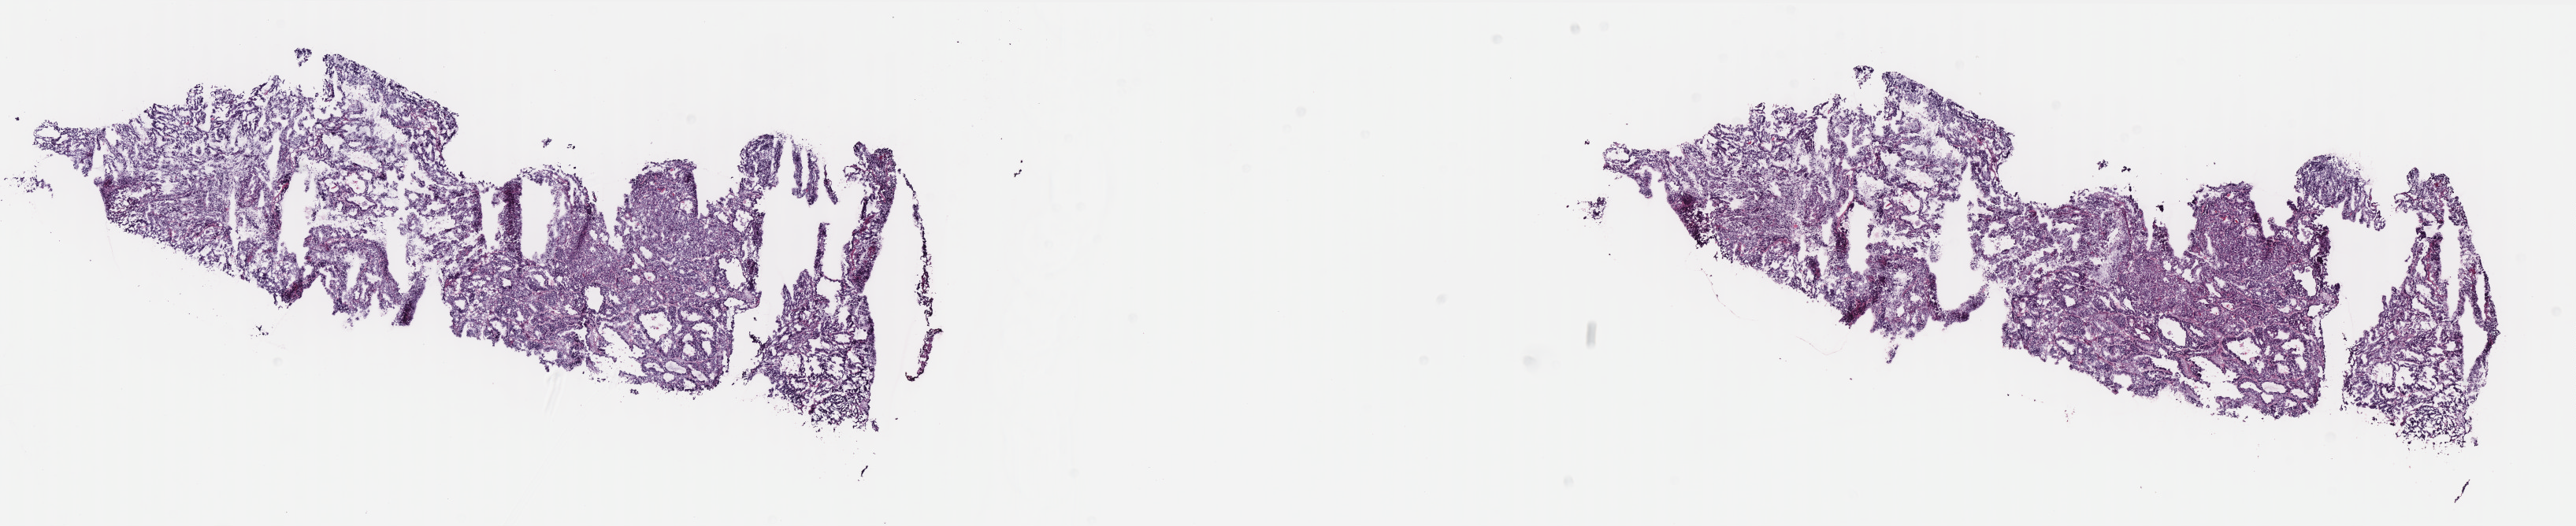
H&E-stained whole-slide image — low-resolution overview of the scanned area, about 26.2 x 5.4 mm (slide scanned at 40x), frozen section from the bottom of the tissue portion, sample: primary tumour, uterus. Female patient; age at initial diagnosis 79 years. Pathologist review of this section (percent, as recorded): tumour cells 100%, tumour nuclei 85%.
Diagnosis: Endometrioid adenocarcinoma, NOS.